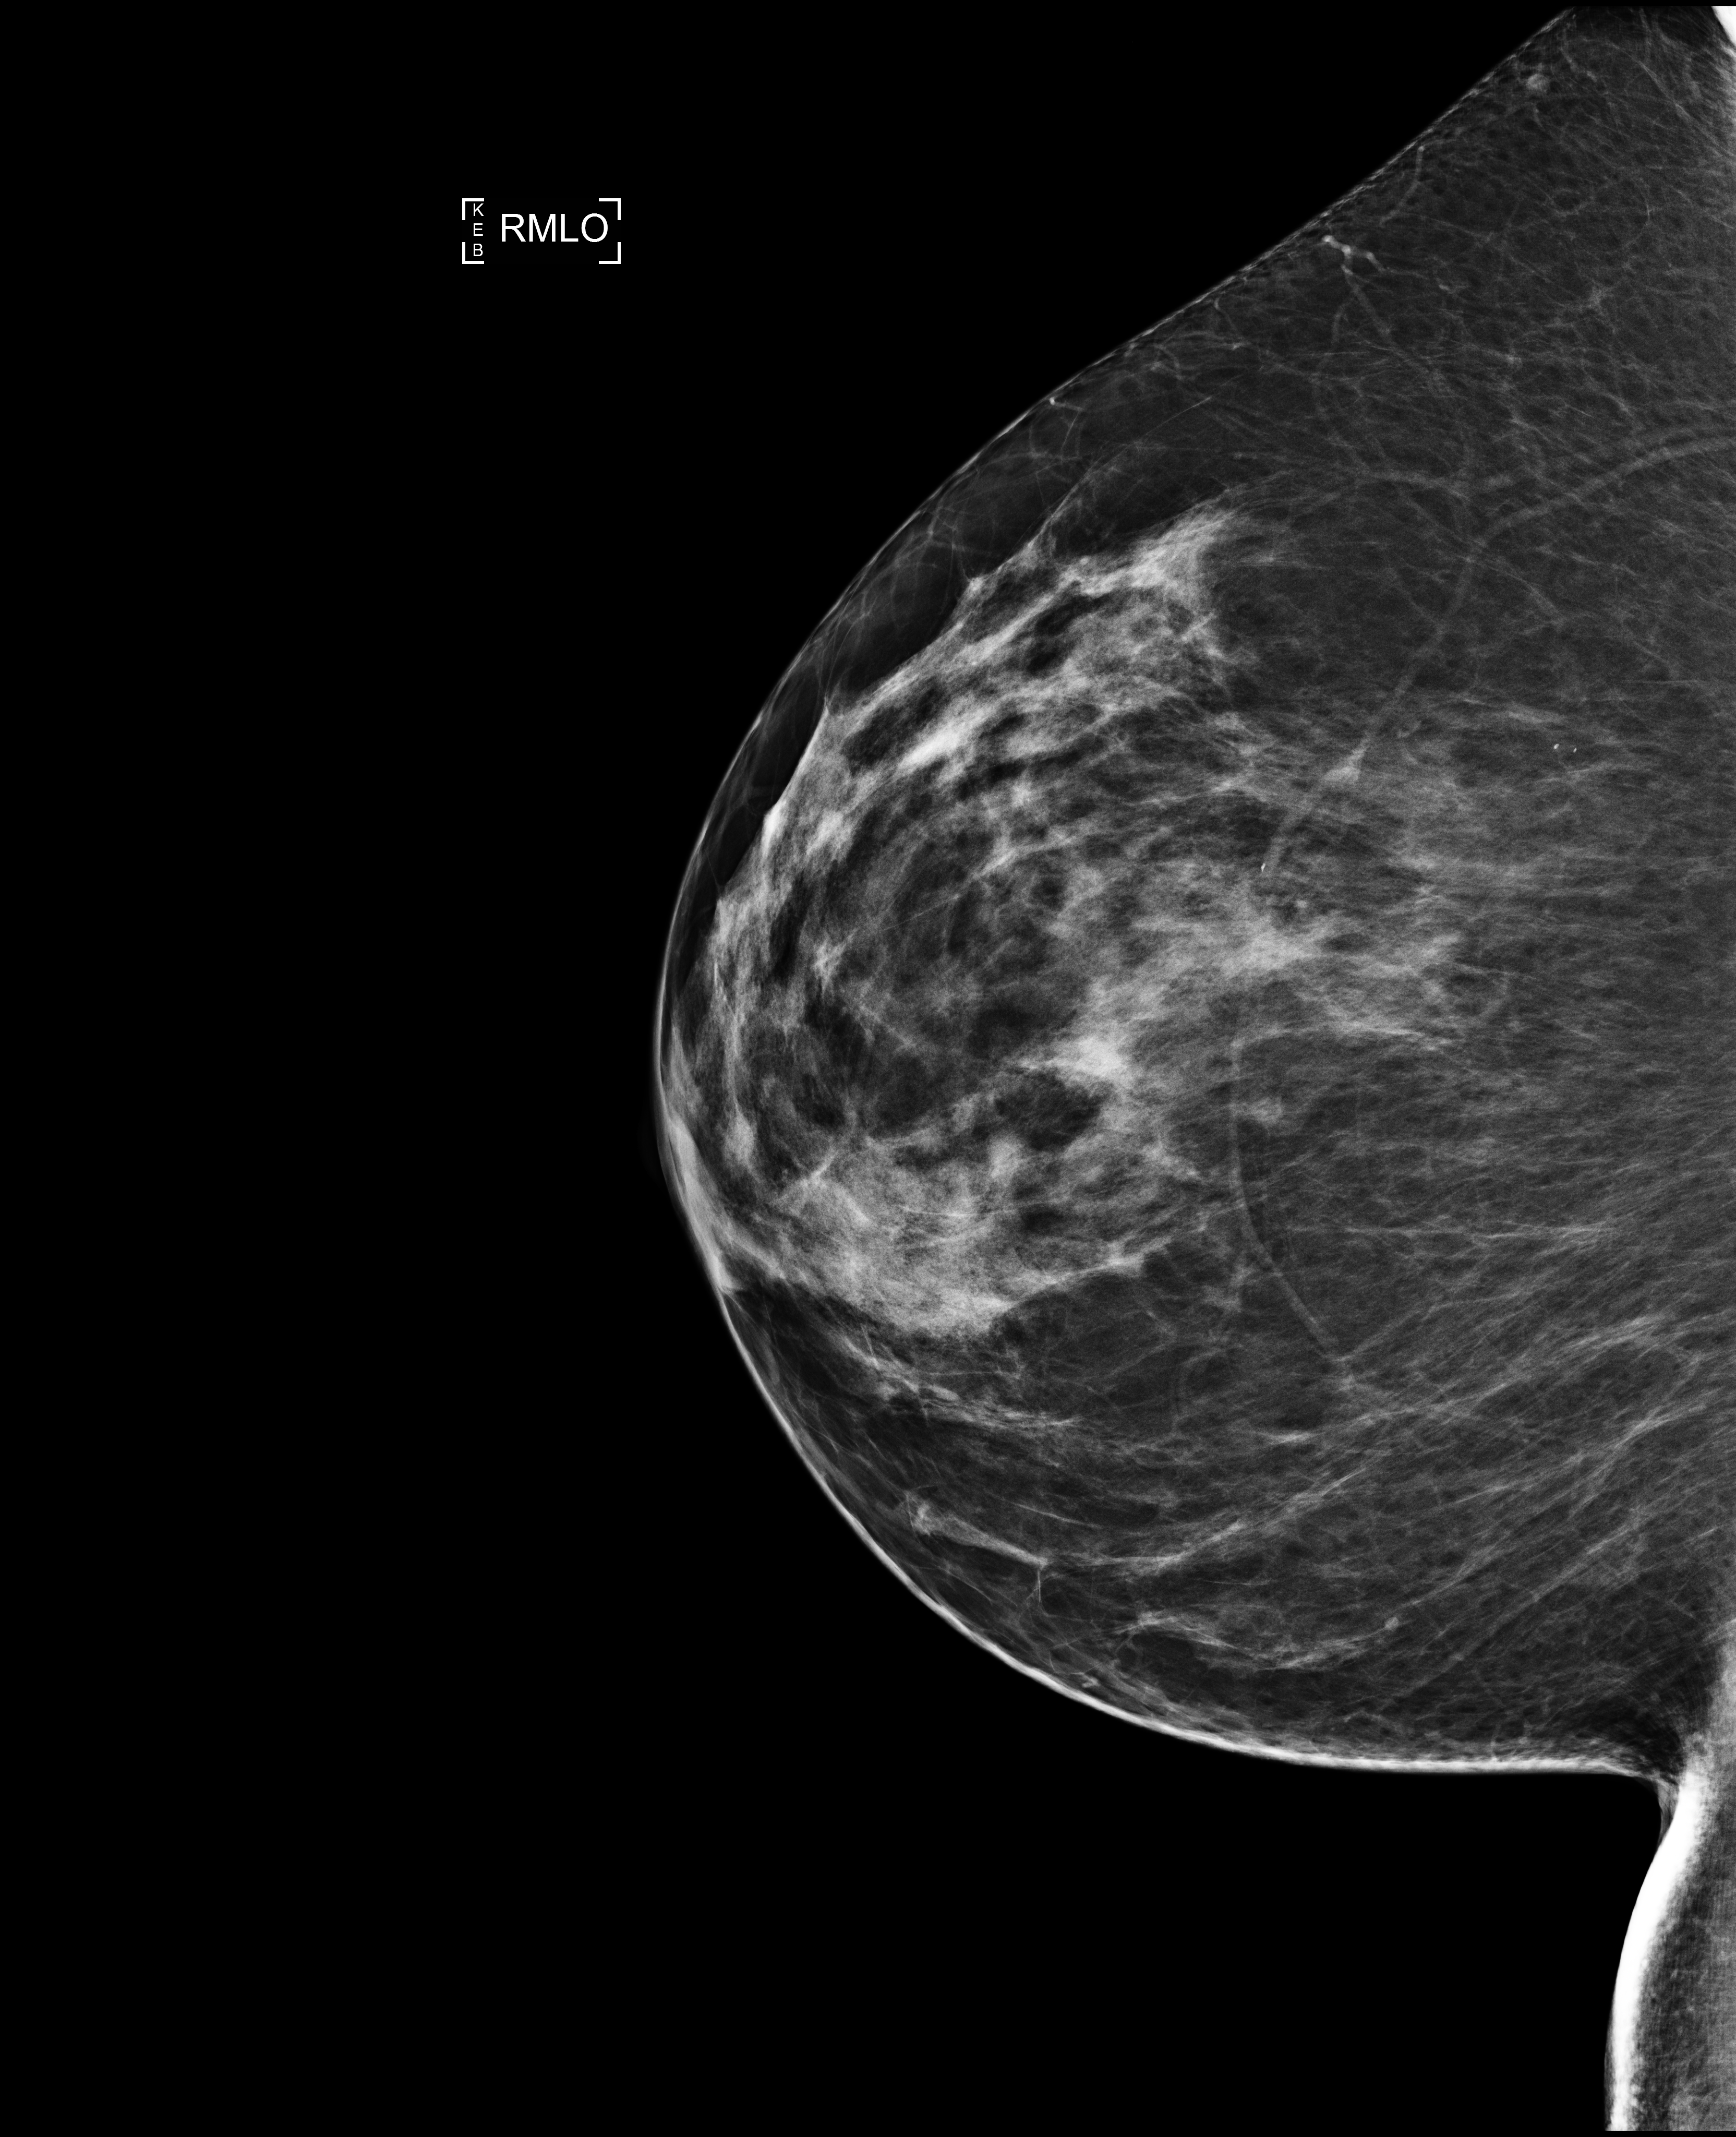
Full-field digital mammogram (FFDM), right breast, MLO view, annual screening mammography examination. Patient: female, 64 years.
BI-RADS breast density category at the screening exam (both breasts, scale 1–4): 3. Final BI-RADS assessment for this screening round (tomosynthesis exam, both breasts): category 1. Recall: no recall after this screen.